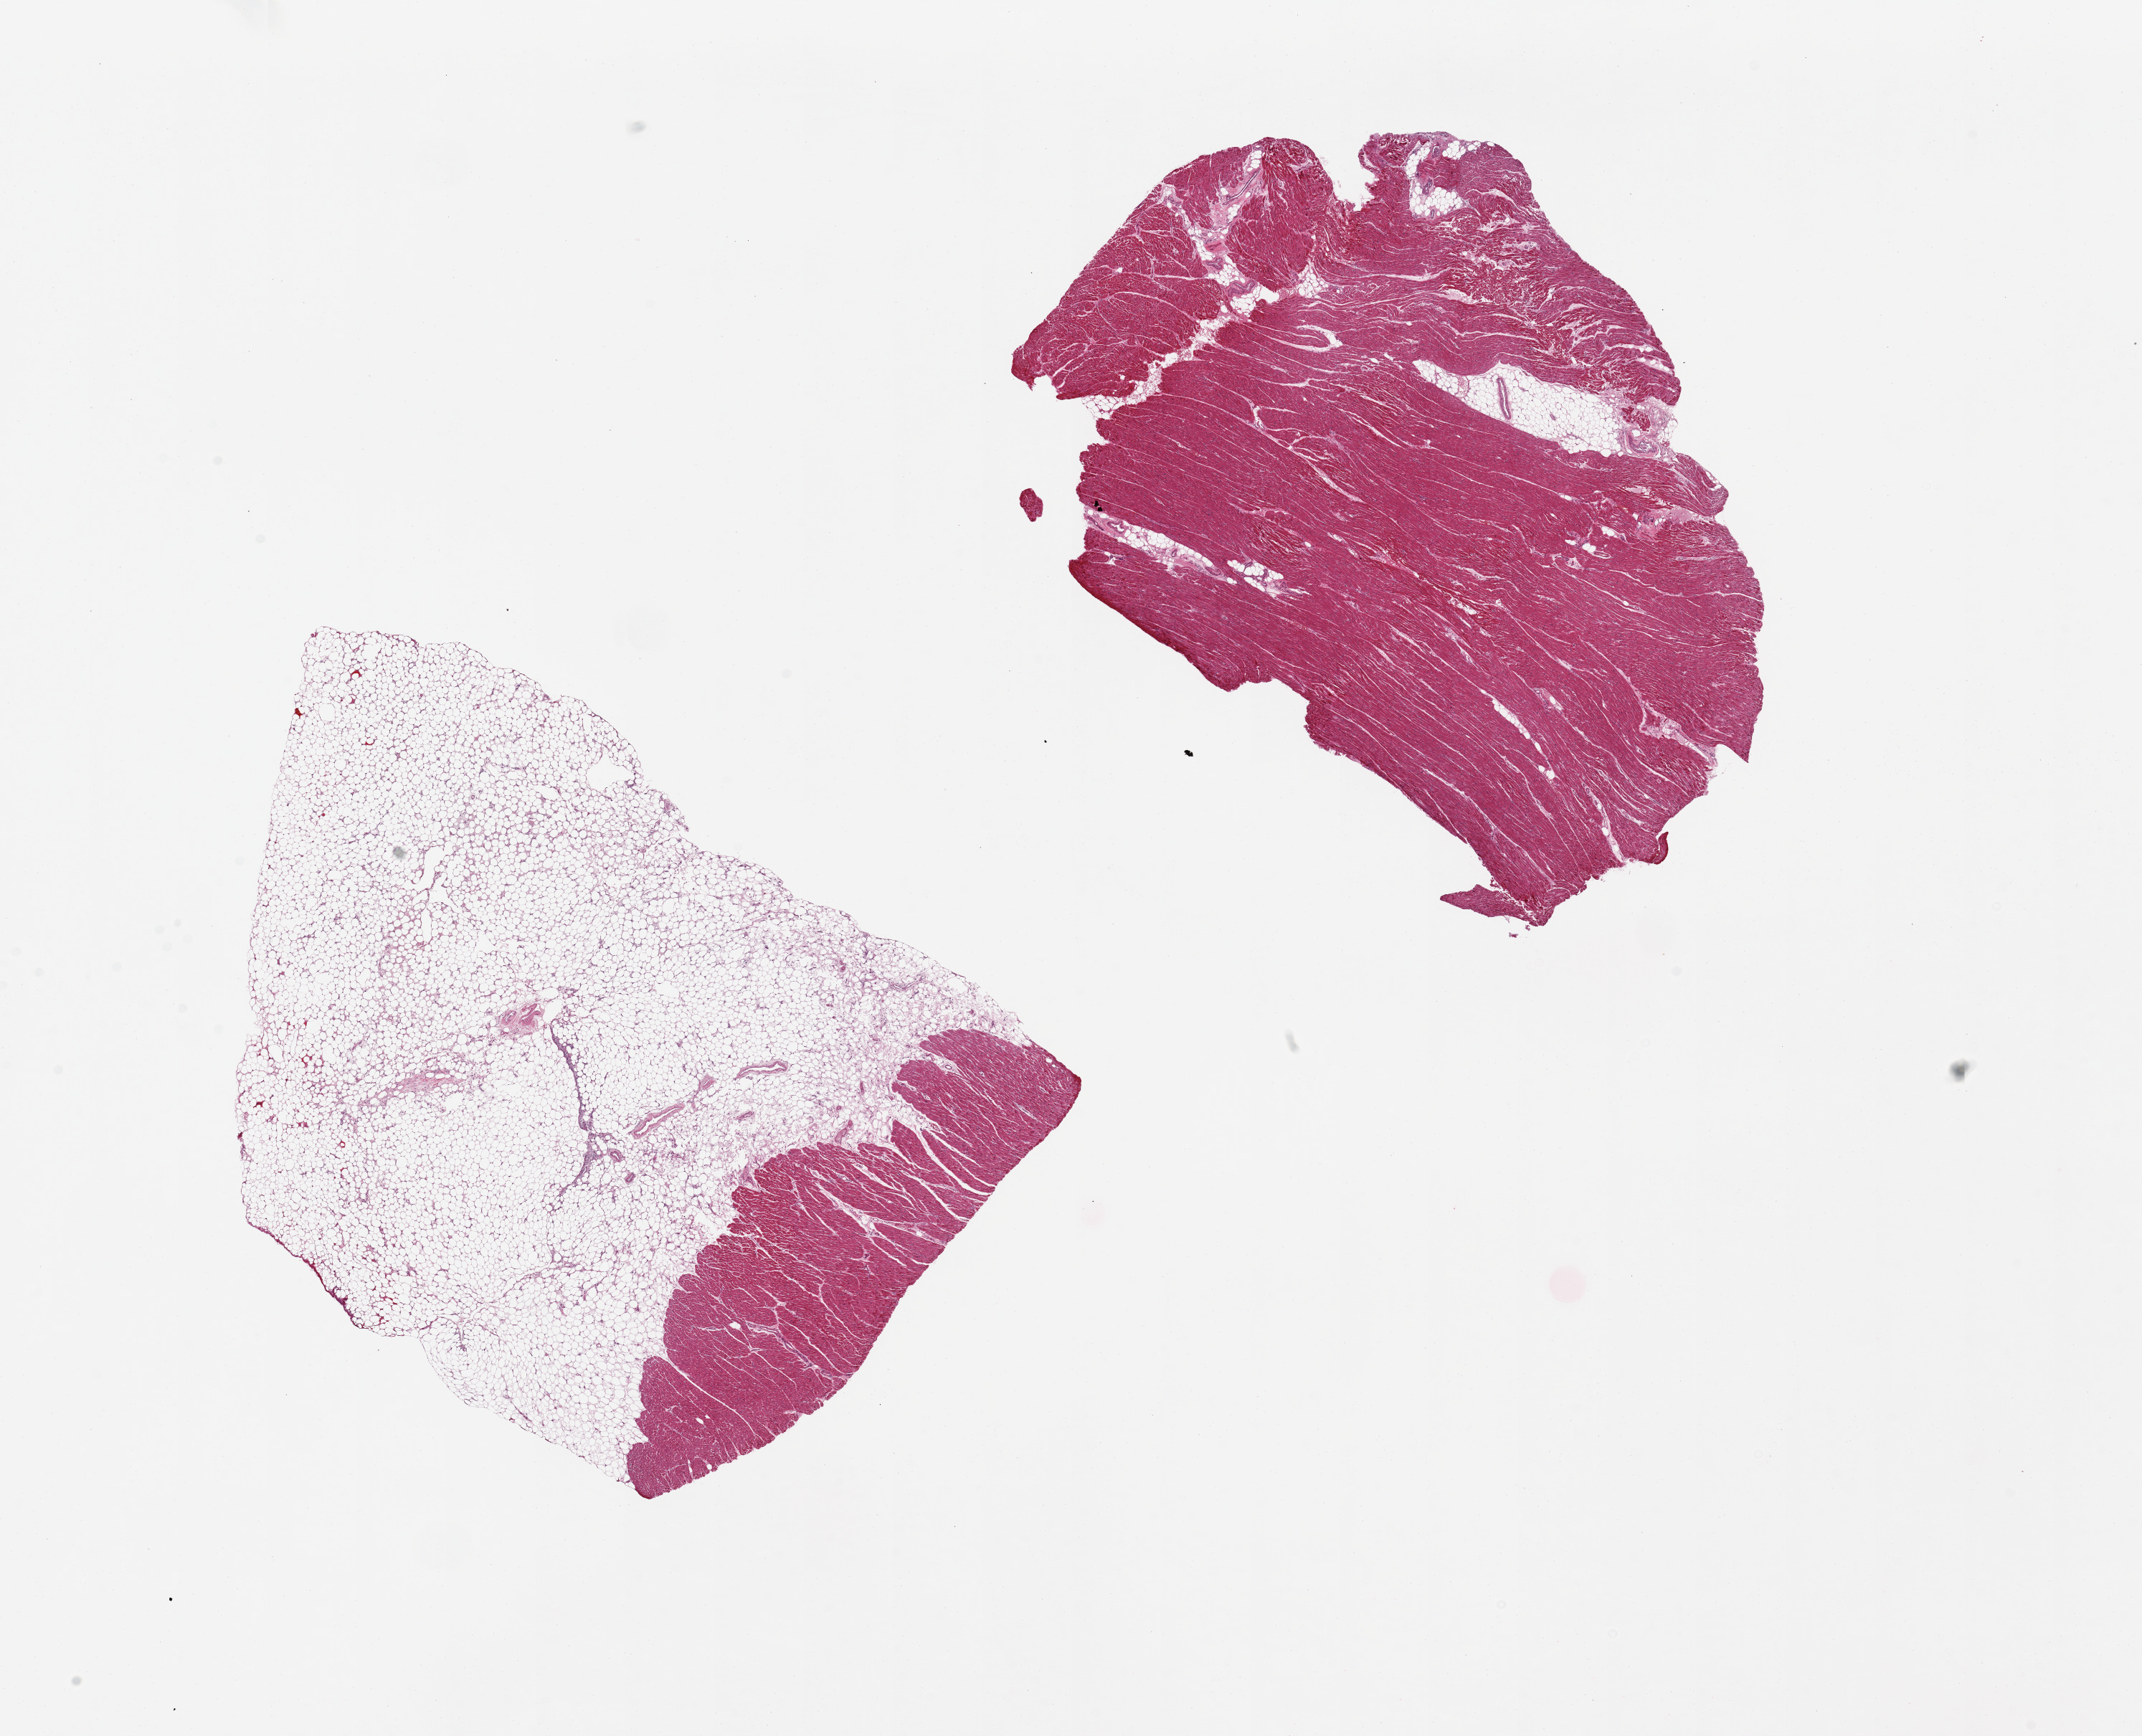
Haematoxylin and eosin whole-slide image, shown as a low-resolution overview of the whole scanned area (about 23.6 x 19.1 mm, from a 20x scan); PAXgene-fixed paraffin-embedded (PFPE) section; sampled site (target tissue): heart; donor tissue sample. Male donor.
- review note (as recorded): 2 pieces, 10x7 & 9x7mm; 1 is 80% external adipose; other has 10% internal adipose; hypertrophied fibers